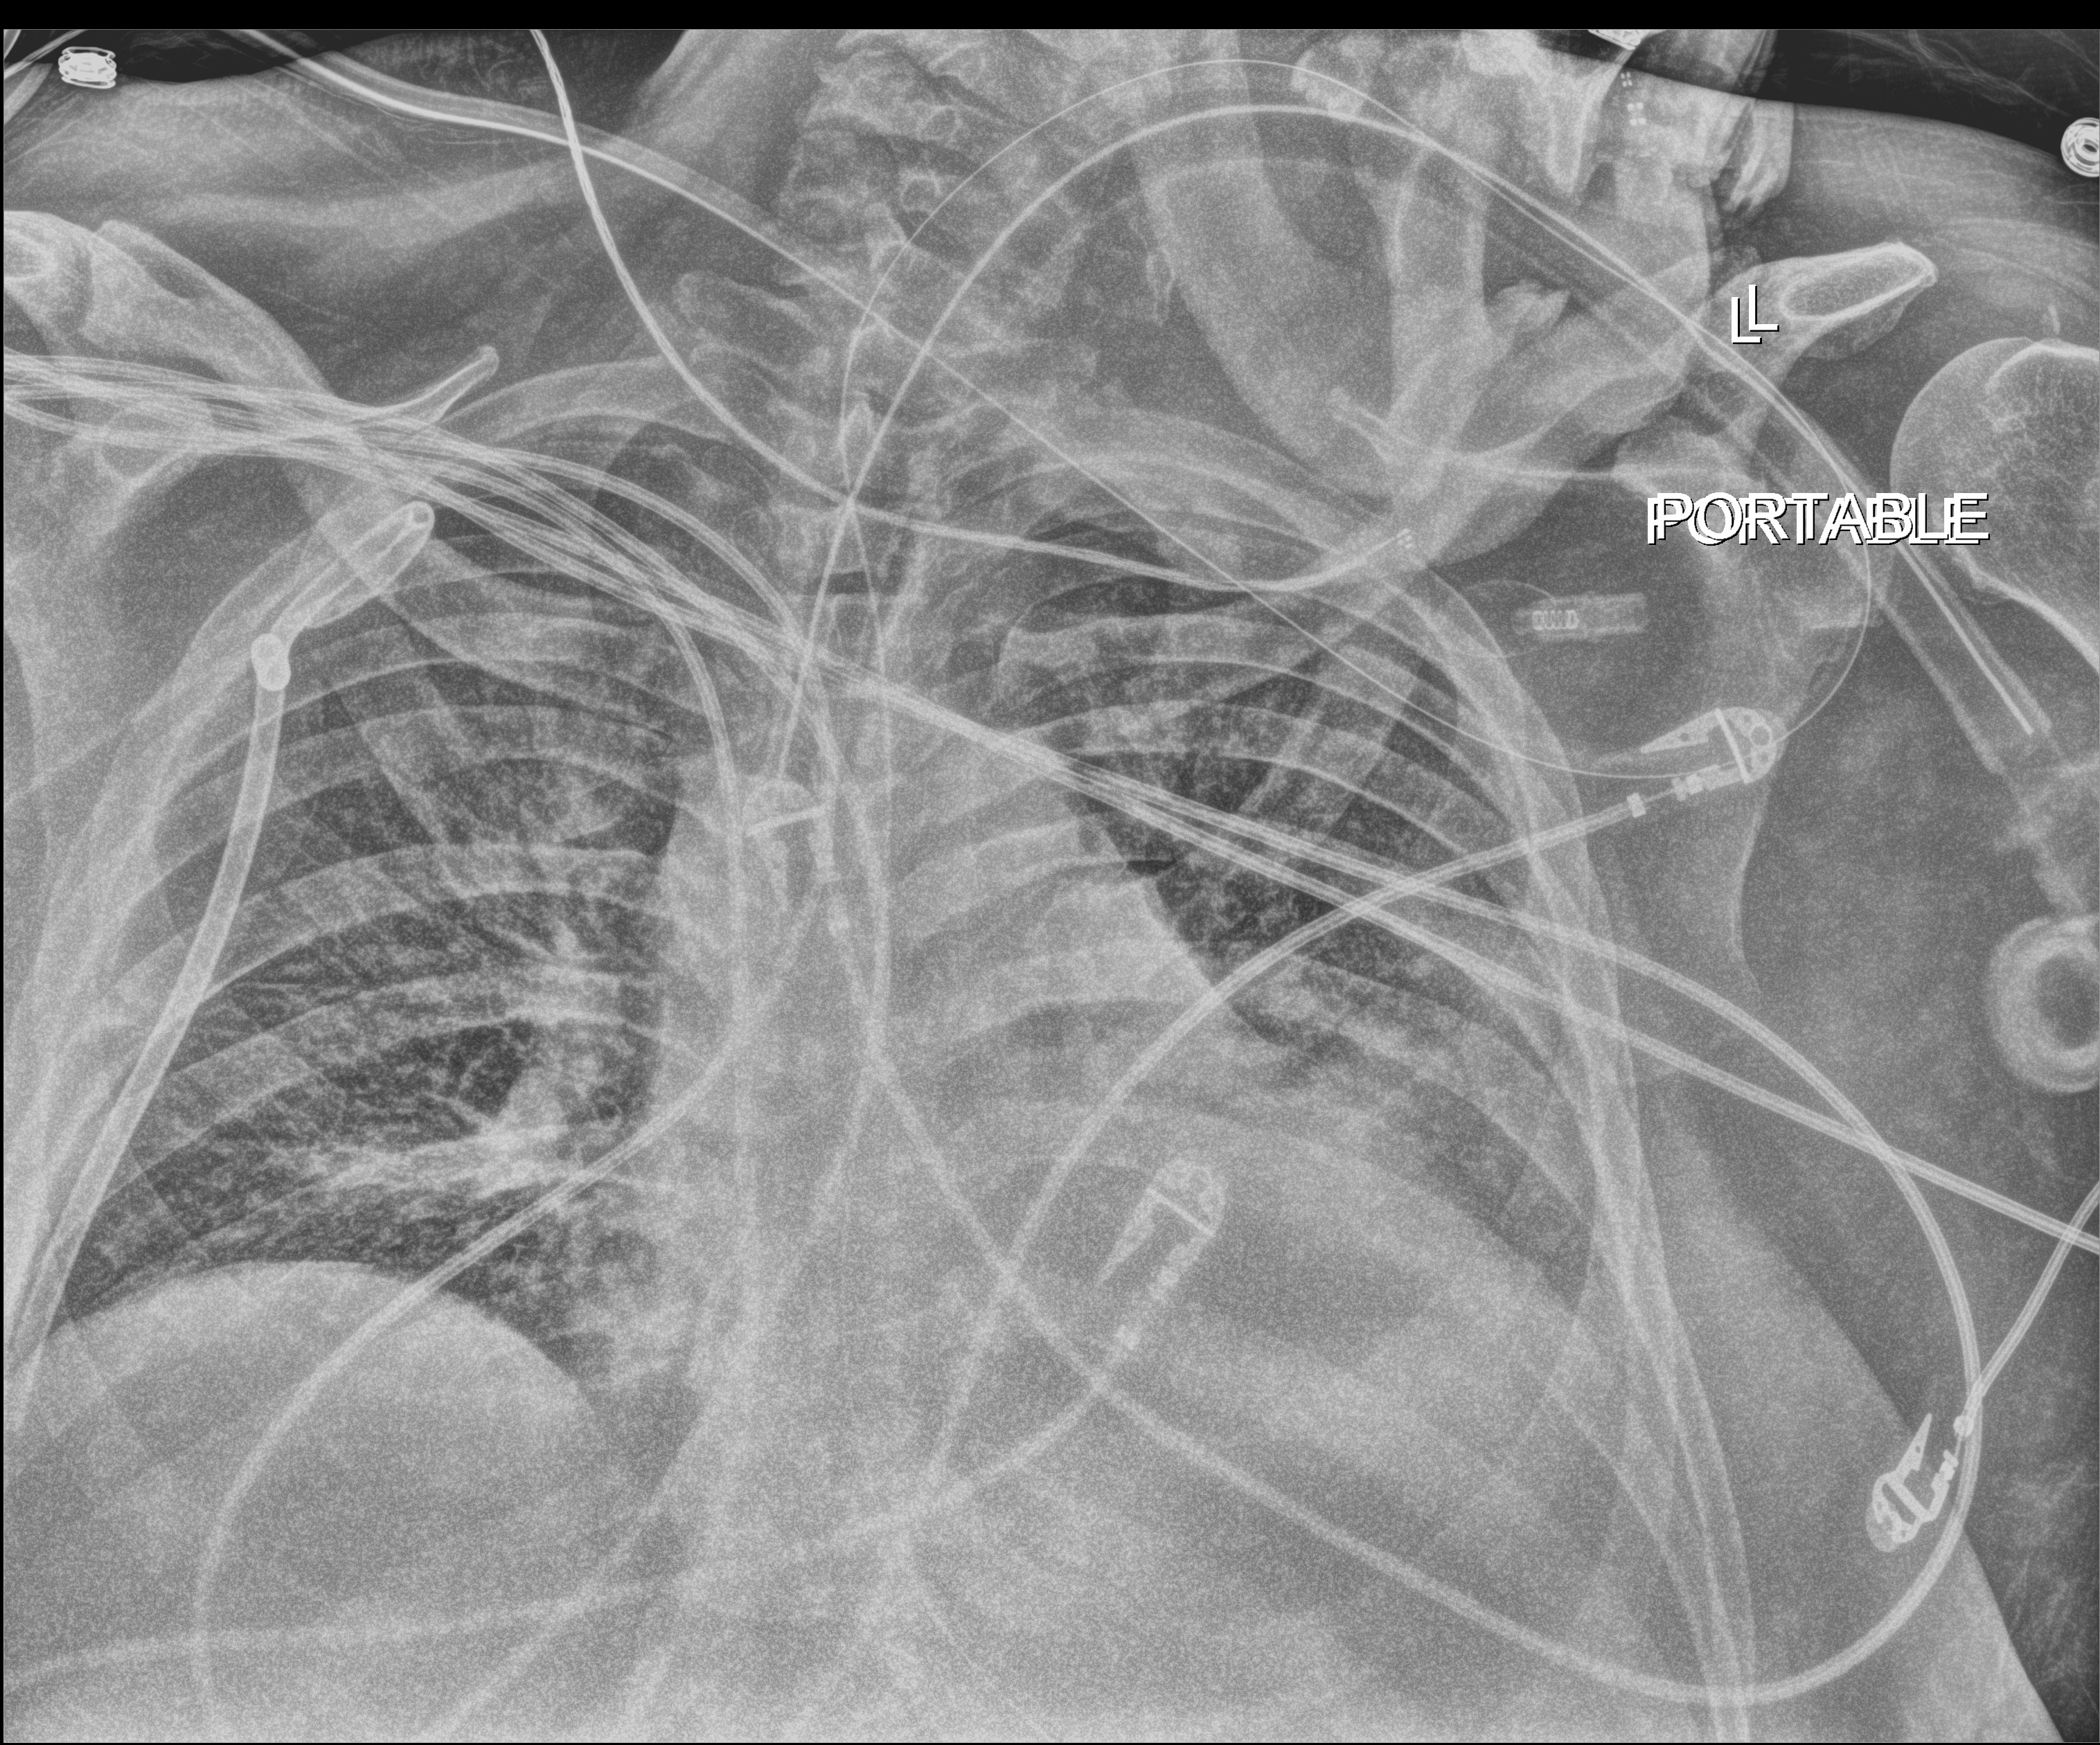
Chest X-ray. Patient hospitalised with COVID-19; male, aged 60–74 years.
Hospital-stay facts (about this admission, not read from this image; timing relative to this image not recorded):
- admitted to intensive care during this hospital stay: yes
- smoking status (admission record): never